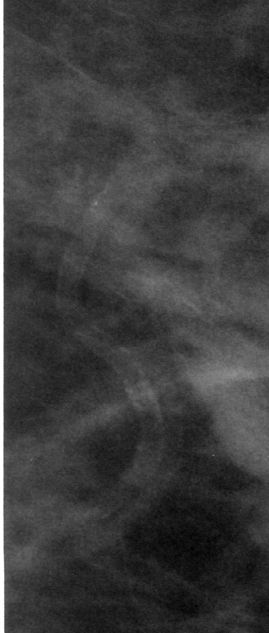
Cropped region of a digitized screen-film mammogram centred on a radiologist-marked abnormality, left breast, CC view, BI-RADS breast density category 2 (scale 1–4).
Marked abnormality: calcifications, morphology vascular; BI-RADS assessment category 2; benign without callback (not worked up further).